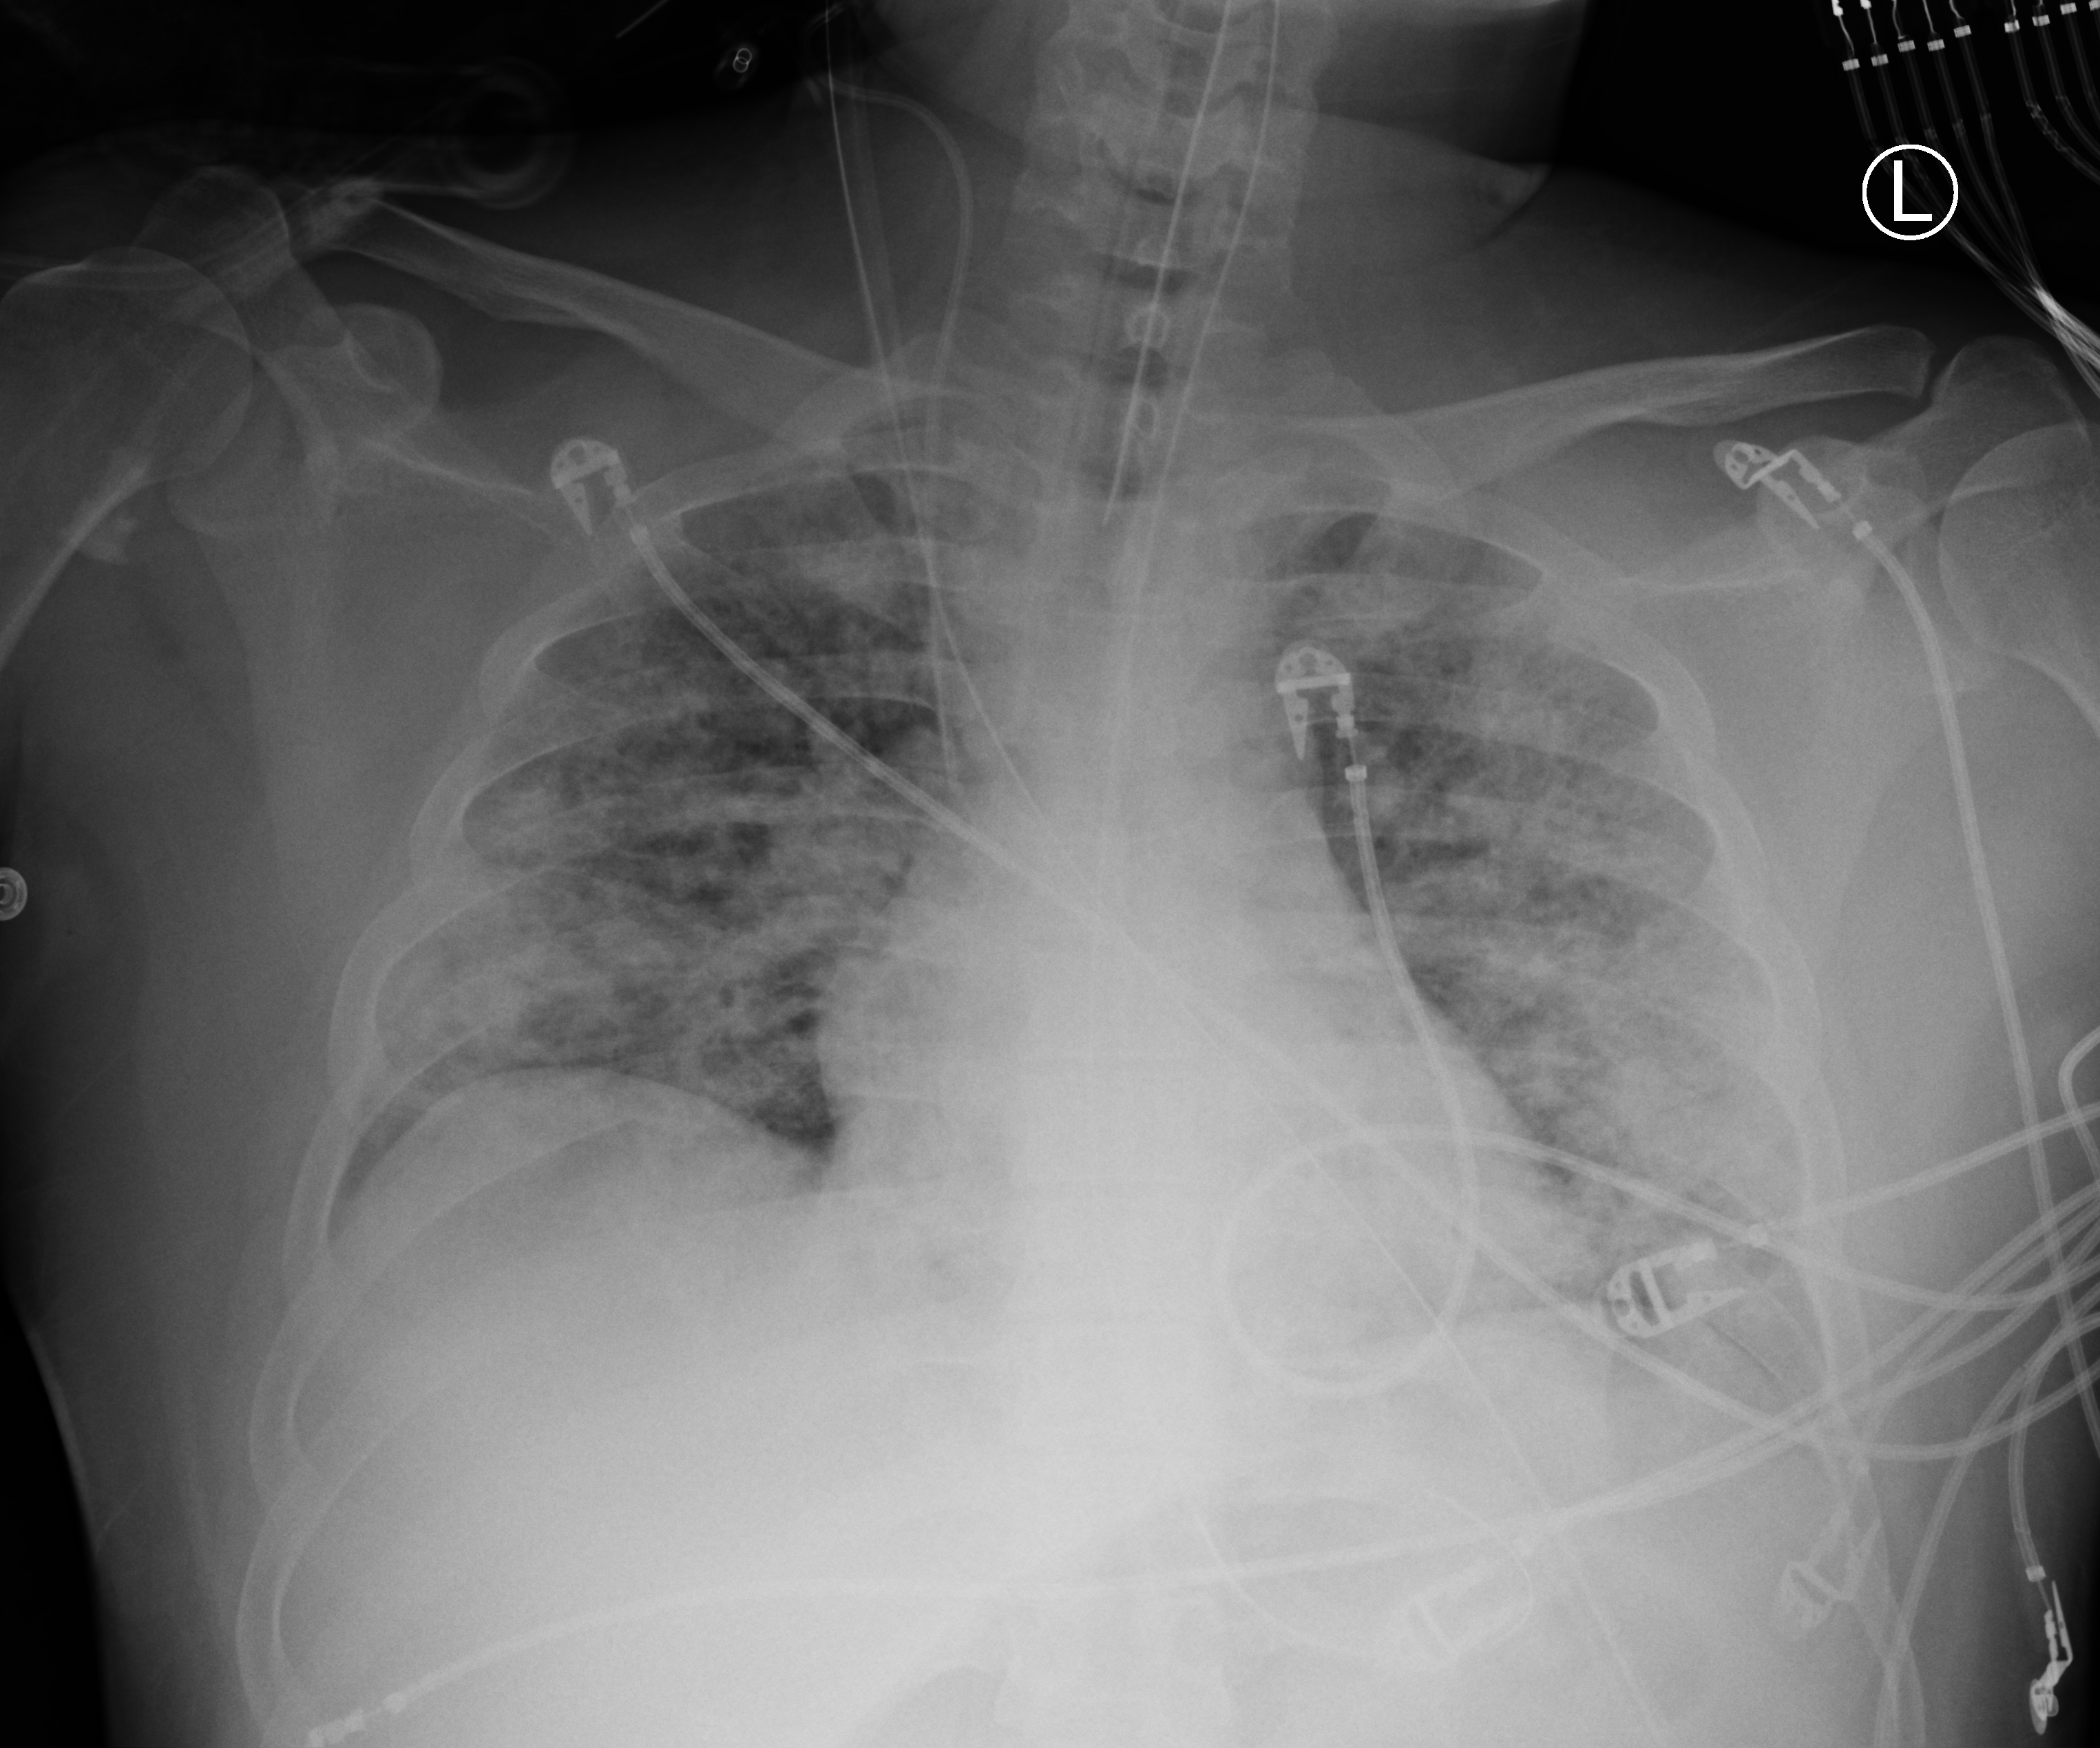
Portable chest radiograph, anteroposterior (AP) projection. Male patient hospitalised with COVID-19, age 18–59 years.
Hospital-stay facts (about this admission, not read from this image; timing relative to this image not recorded): mechanically ventilated during this hospital stay: yes; diabetes (admission record): yes; admitted to intensive care during this hospital stay: yes.